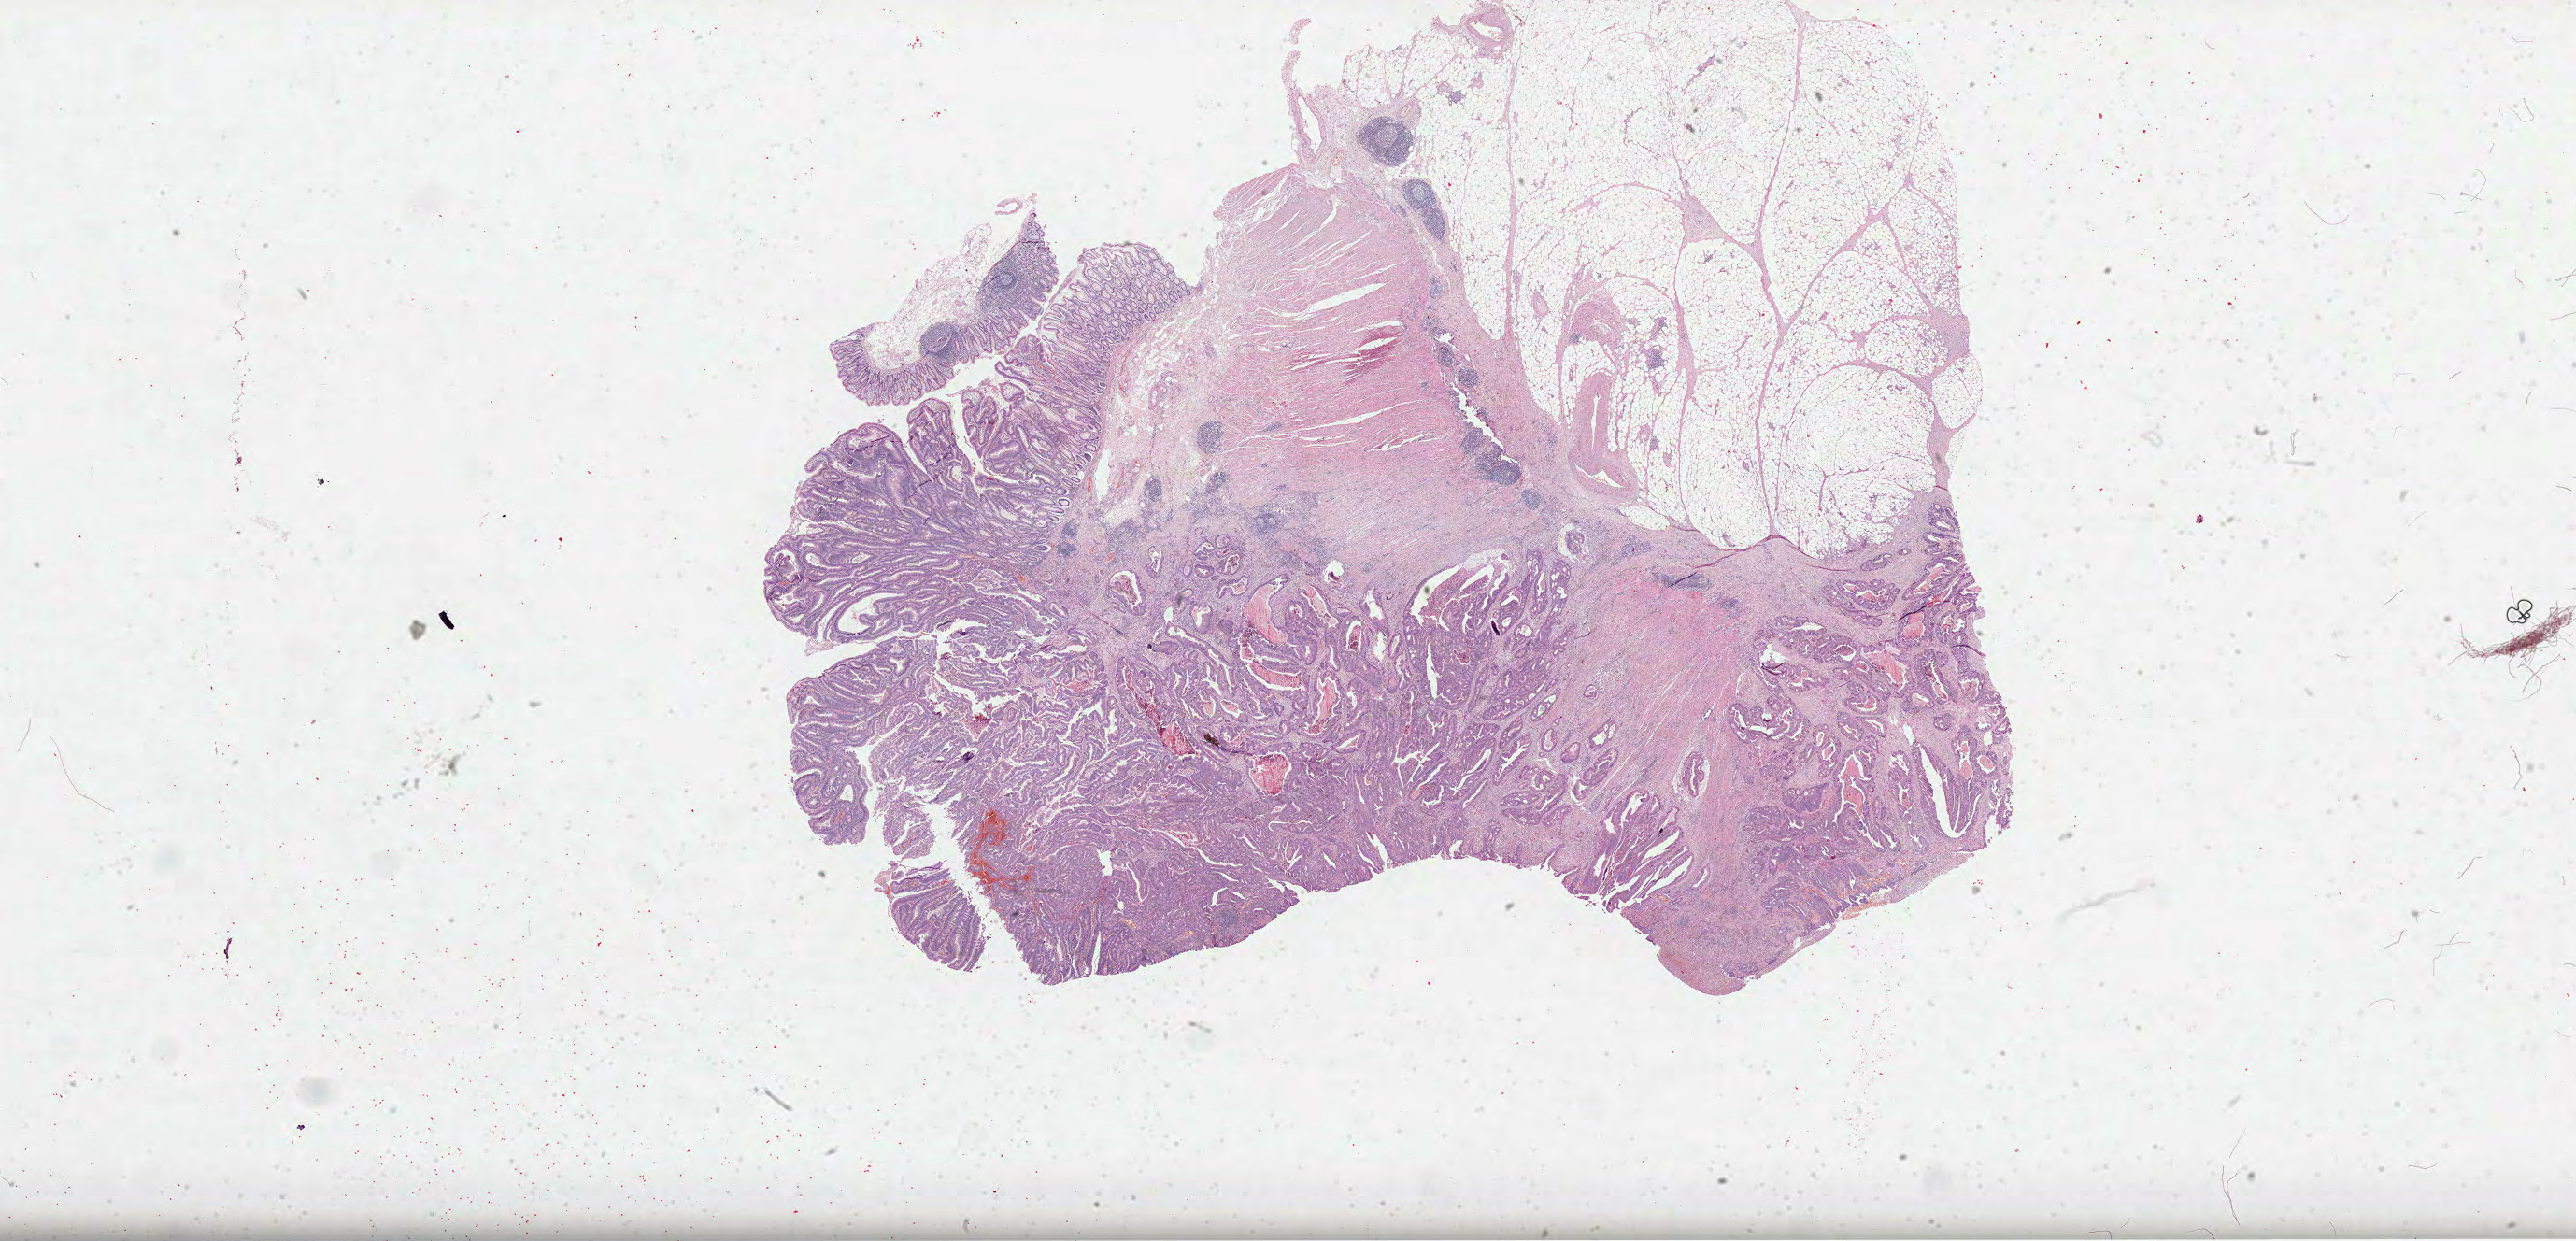
H&E-stained whole-slide image — low-resolution overview of the scanned area, about 44.5 x 21.4 mm, formalin-fixed paraffin-embedded (FFPE) diagnostic section, sample: primary tumour, colon. Male, age 83 years at initial diagnosis.
Pathologic diagnosis: Adenocarcinoma, NOS. Lymph nodes positive (case pathology): 7 of 10 examined.